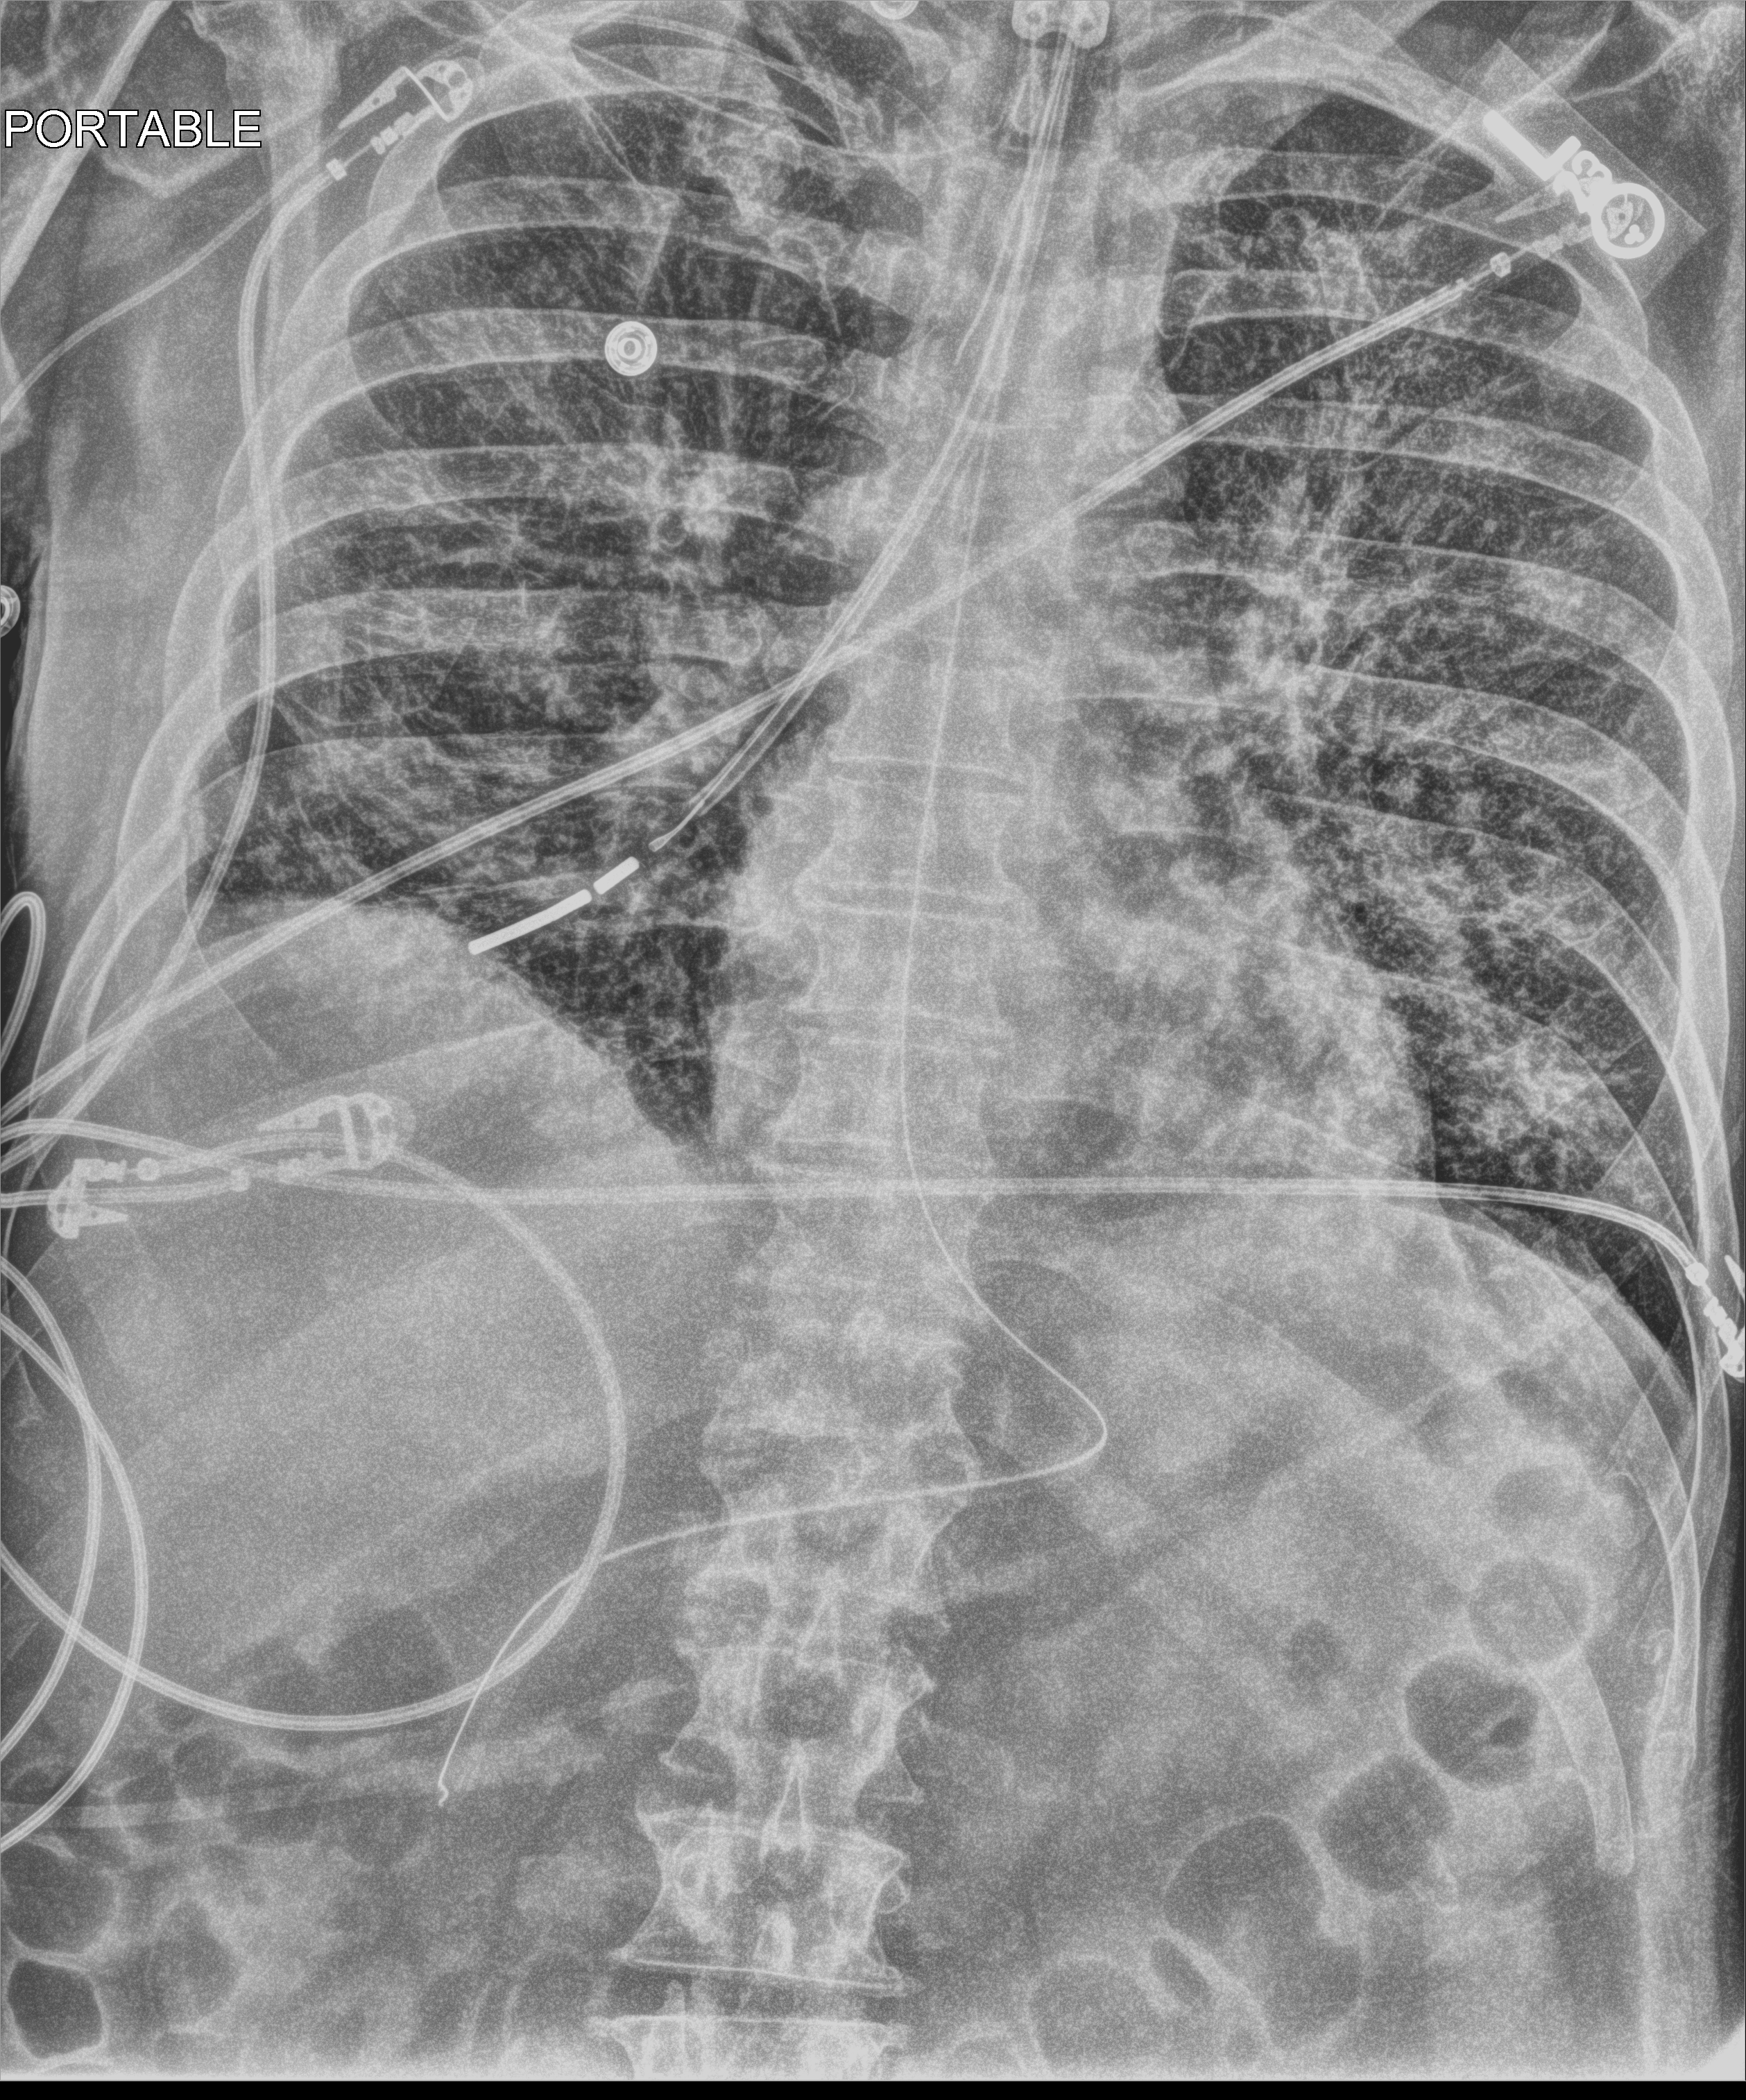
Portable chest radiograph, anteroposterior (AP) projection. Patient hospitalised with COVID-19; male, aged 60–74 years.
Hospital-stay facts (about this admission, not read from this image; timing relative to this image not recorded): length of hospital stay: 43 days; mechanically ventilated during this hospital stay: yes; admitted to intensive care during this hospital stay: yes.